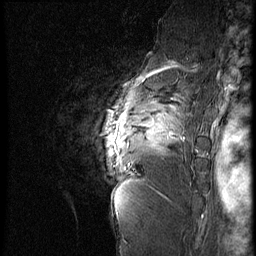
Breast MRI (dynamic contrast-enhanced), one sagittal slice; slice 53 of 60 in the series (ordered by position); 4 images stored at this slice position (order not interpretable as contrast timing); 1.5 T; TE 4.2 ms, TR 9 ms; 2.5 mm slice thickness; 256 × 256 image matrix. Patient: female, 56 years. From the clinical record (not read from this slice): setting: breast cancer imaged before/during neoadjuvant chemotherapy; receptor status: HER2-positive.
Outlined on this slice (semi-automatically segmented with operator editing):
- analysis volume of interest (the breast-tissue region the enhancement analysis was run in; not a lesion): bounding box (x1, y1, x2, y2) in pixels: (83, 83, 199, 177)
- tumour enhancement mask (voxels above the 140 % enhancement threshold inside the analysis volume of interest): (113, 116, 169, 145)